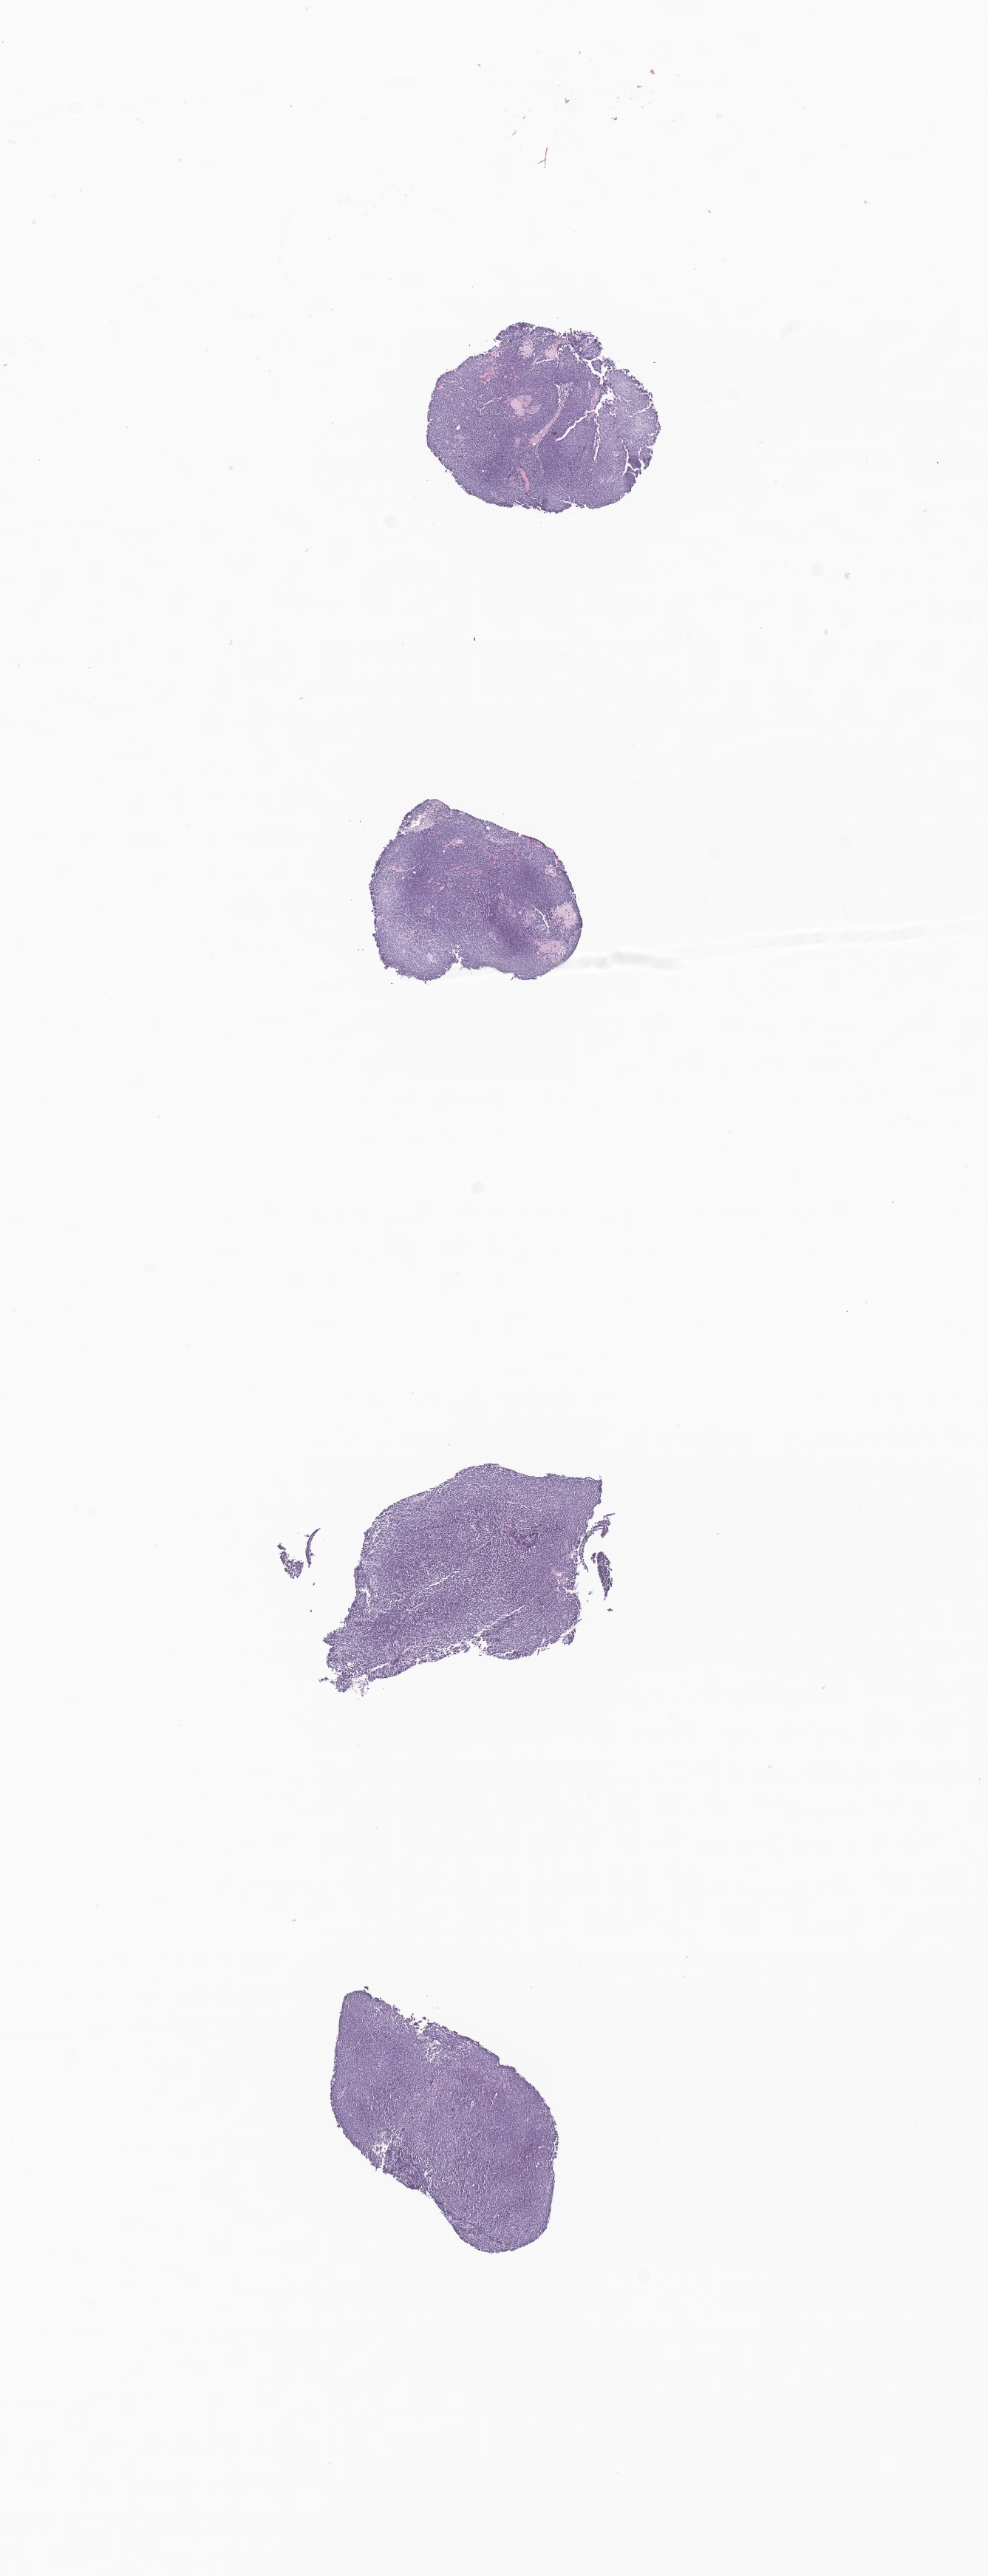
Whole-slide image, hematoxylin and eosin (H&E) stain of tumor tissue from the brain, low-resolution overview of the scanned area, about 5.6 x 14.7 mm. FFPE section. Male patient, age 210 months (17 years 6 months).
Diagnosis: Pineoblastoma.